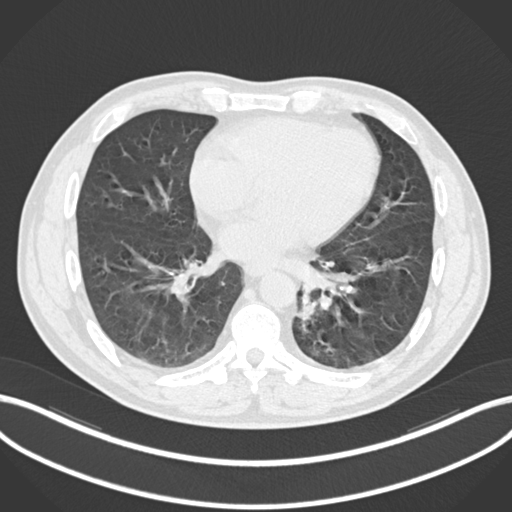
Chest CT, one axial slice. Slice 82 of 223 in the series (ordered by position). 120 kVp. Lung window (W 1500 / L -600 HU). 1 mm slice thickness. 512 × 512 image matrix, field of view 400 × 400 mm. Male patient, age 50 years. Case-level facts recorded for this patient, not image findings: clinical TNM (as recorded): T2a N3 M0.
Structures marked on this image (rectangle marked by the reading radiologist):
- lung tumour (recorded histology: squamous cell carcinoma): box from (x=294, y=288) to (x=321, y=327) px